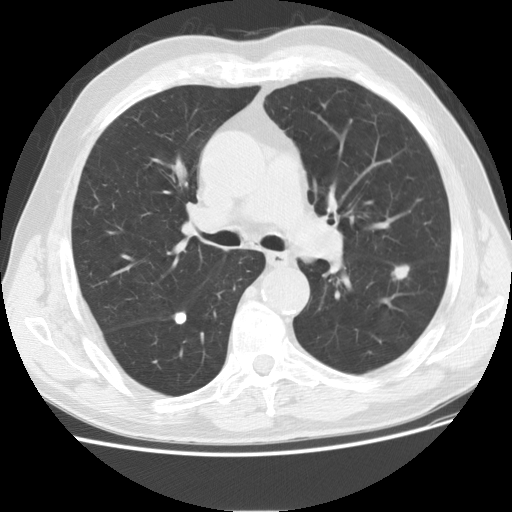
Low-dose screening chest CT, one axial slice. Position 112 of 175 along the scan axis. Lung window (W 1500 / L -600 HU). 2.5 mm slice thickness. 512 × 512 image matrix, field of view 360 × 360 mm.
Outlined on this slice (outlined manually by an expert reader):
- lesion 1 (tumor, lower lobe of left lung): bounding box (x1, y1, x2, y2) in pixels: (392, 265, 410, 280)